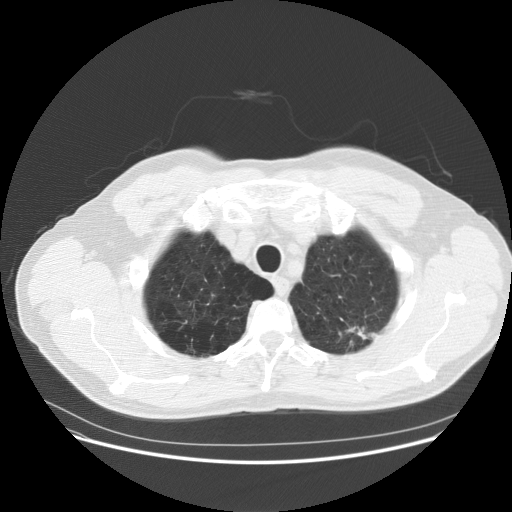
Chest CT (low-dose screening protocol), one axial image. First (baseline) screen. Lung window (W 1500 / L -600 HU). Standard (soft-tissue) reconstruction kernel (STANDARD). Slice 16 of 158 in the series. 512 × 512 image matrix. Male participant, aged 61 years at enrolment. Current smoker at enrolment.
Expert reader's lesion annotation, bounding box <329,310,396,366> (left, top, right, bottom; pixels). Reader record for this screening exam (exam-level; its link to the box is not recorded): non-calcified nodule or mass ≥4 mm, left upper lobe, 12 × 6 mm, poorly defined margins, soft tissue attenuation. Official screen result: positive, change unspecified: nodule(s) >= 4 mm or enlarging nodule(s), mass(es), or other non-specific abnormalities suspicious for lung cancer. Participant outcome: lung cancer diagnosed 317 days after this screen — adenocarcinoma, NOS, left upper lobe, poorly differentiated (G3), stage IIIA (AJCC 6th edition), 30 mm at pathology.